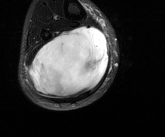
MRI of an extremity soft-tissue mass, one axial slice; position 55 of 81 along the scan axis; T2-weighted fat-saturated; MR volume resampled by the dataset authors to the PET/CT grid (not the native acquisition matrix); 3.27 mm slice thickness; 165 × 137 image matrix, field of view 161 × 134 mm. Male patient. From the clinical record (not read from this slice): histological type: liposarcoma - round cell; grade: high; site of the primary tumour: right calf.
Outlined on this slice (expert contour drawn on MRI and transferred to this co-registered scan by the dataset authors):
- gross tumour volume (mass): box from (x=28, y=25) to (x=108, y=99) px